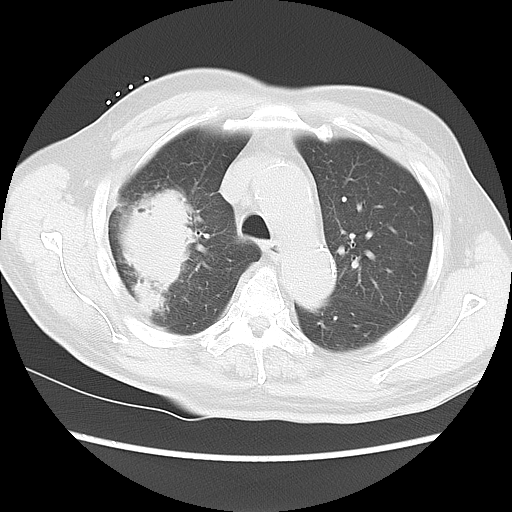
Chest CT, one axial slice; slice 13 of 15 in the series (ordered by position); reconstruction kernel LUNG; 120 kVp; lung window (W 1500 / L -600 HU); 5 mm slice thickness; 512 × 512 image matrix, field of view 350 × 350 mm. Male patient, age 68 years. Case-level facts recorded for this patient, not image findings: clinical TNM (as recorded): T4 N3 M0.
Structures marked on this image (bounding box drawn by a radiologist):
- lung tumour (recorded histology: squamous cell carcinoma): bounding box (x1, y1, x2, y2) in pixels: (113, 181, 201, 311)